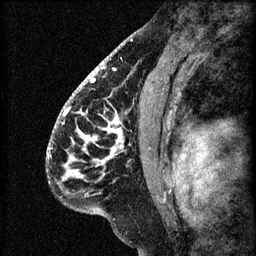
Breast MRI (dynamic contrast-enhanced), one sagittal slice. Position 38 of 60 along the scan axis. 3 images stored at this slice position (order not interpretable as contrast timing). 1.5 T. TE 4.2 ms, TR 8.2 ms. 2.2 mm slice thickness. 256 × 256 image matrix, field of view 180 × 180 mm. Patient: female, 41 years.
Structures marked on this image (semi-automatically segmented with operator editing):
- analysis volume of interest (the breast-tissue region the enhancement analysis was run in; not a lesion): bounding box (x1, y1, x2, y2) in pixels: (56, 104, 157, 207)
- tumour enhancement mask (voxels above the 70 % enhancement threshold inside the analysis volume of interest): (63, 108, 122, 171)